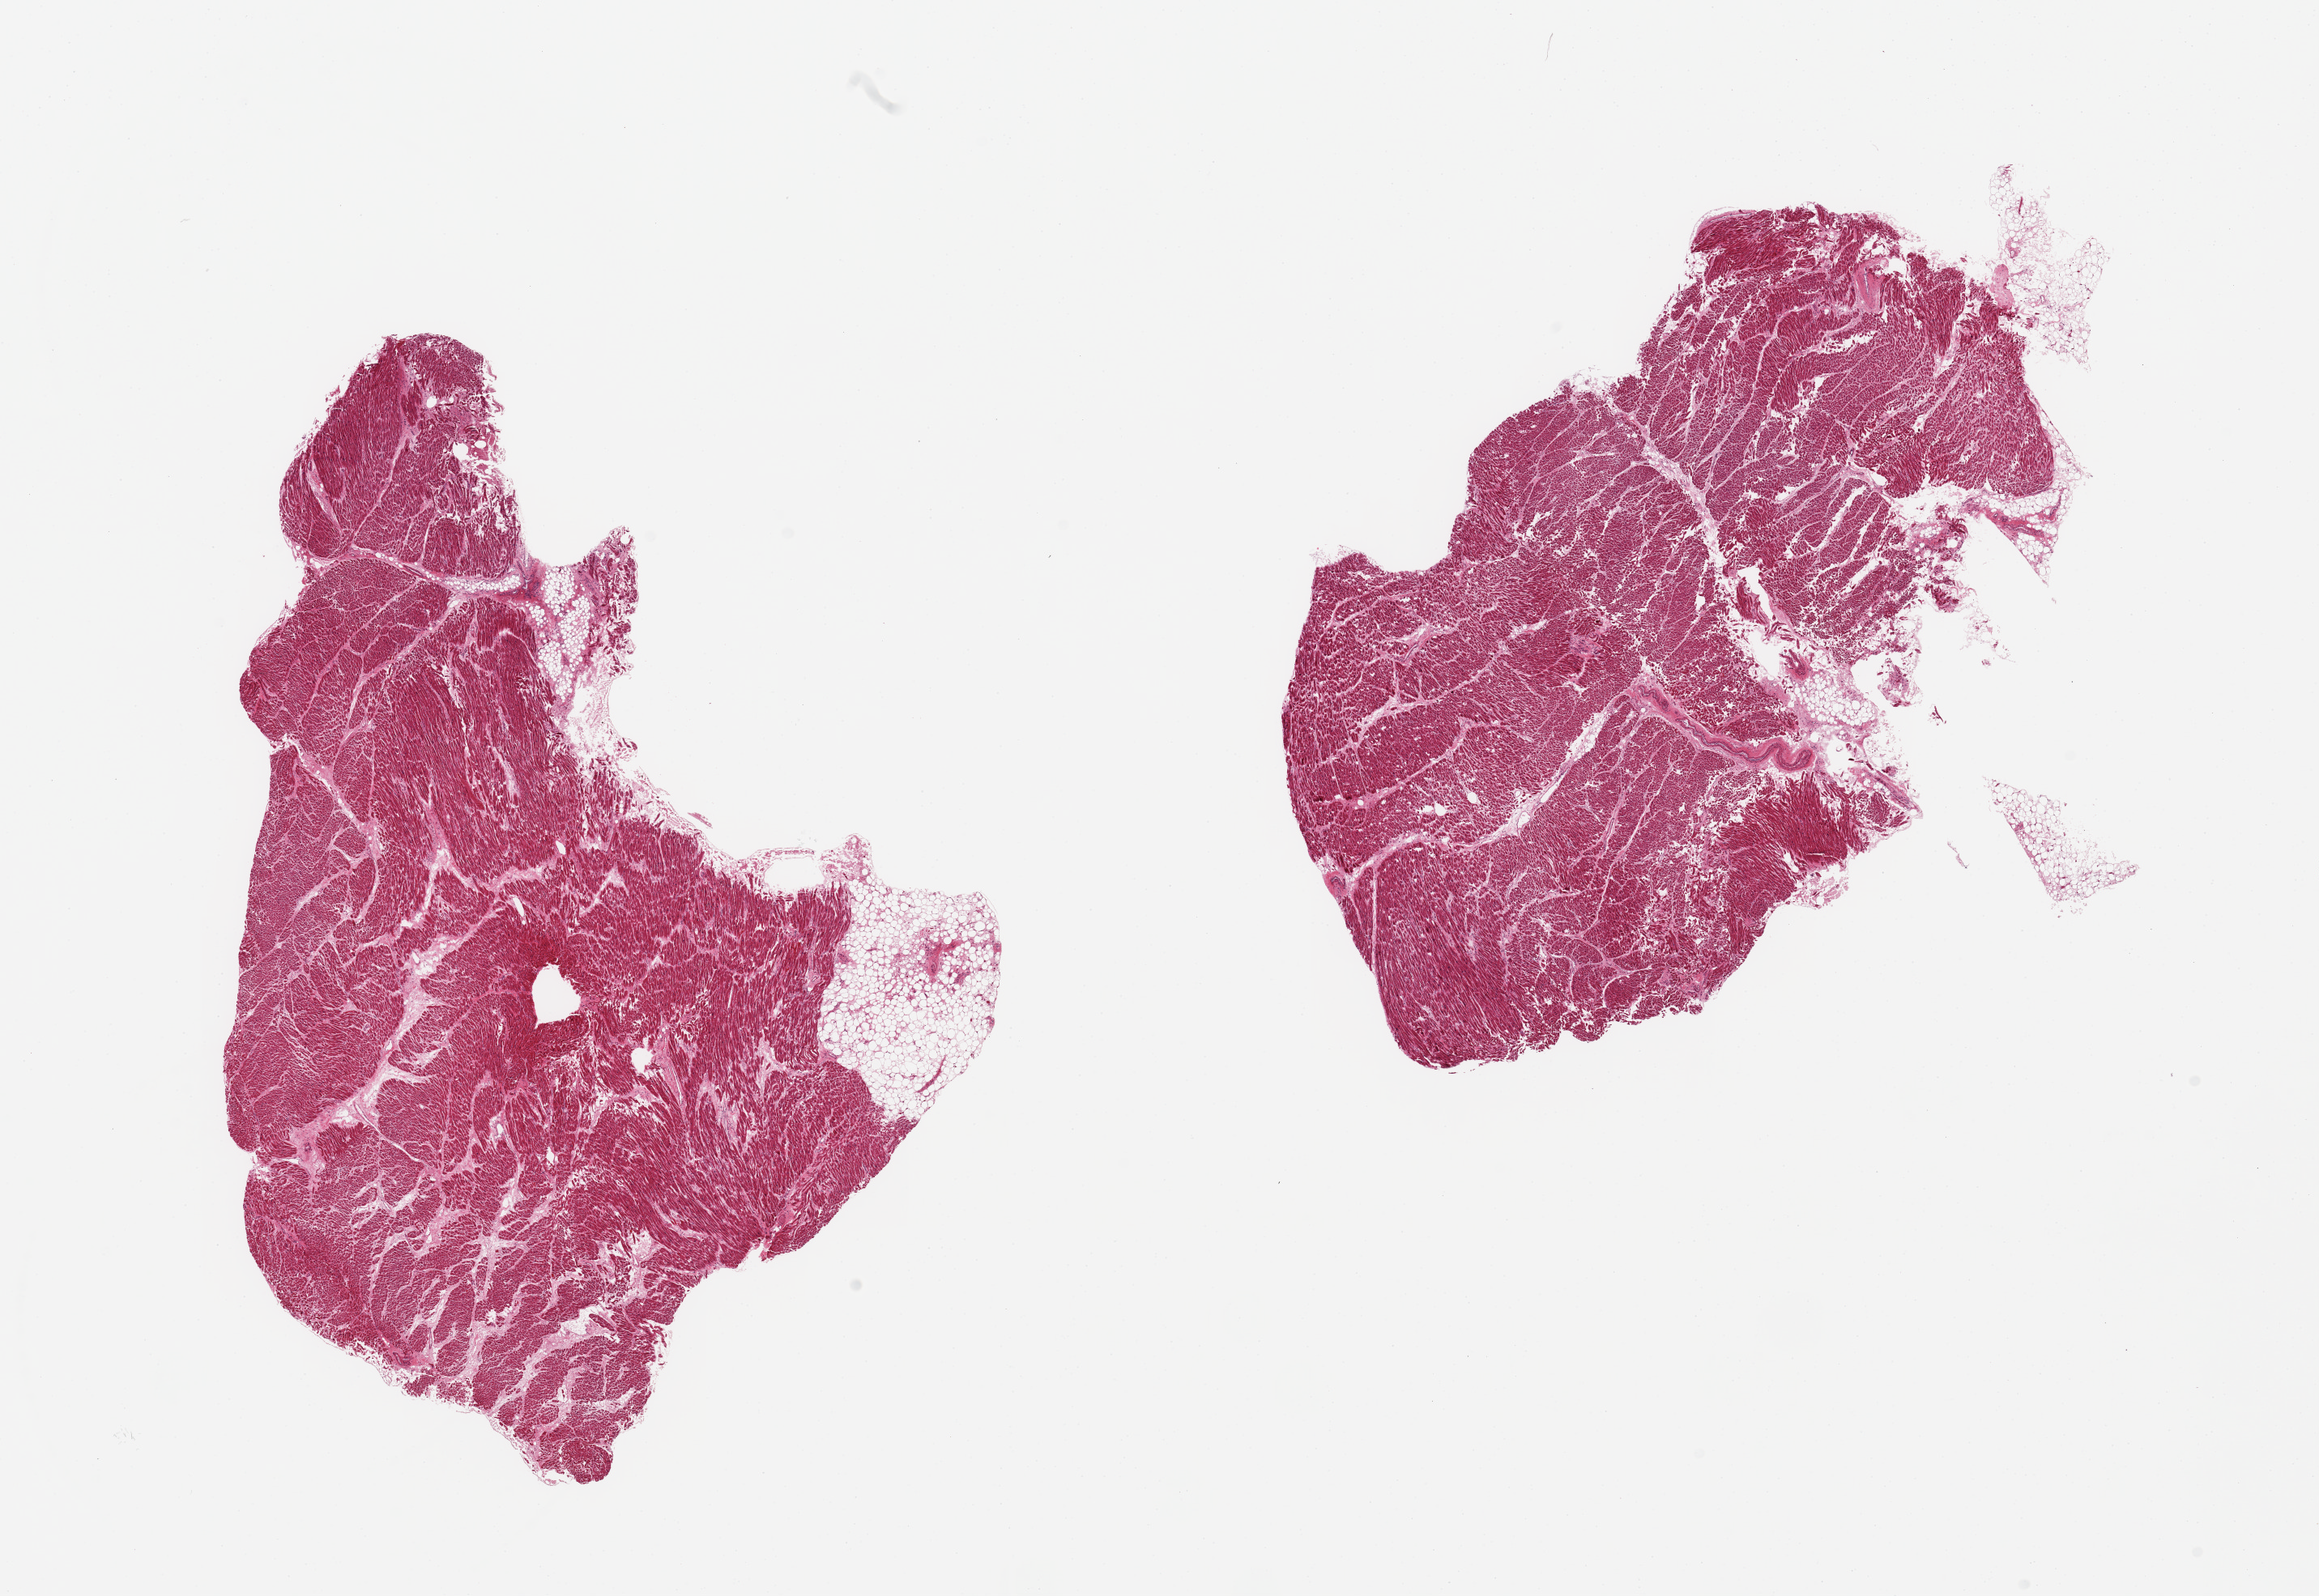
Hematoxylin and eosin (H&E) whole-slide image, brightfield, whole scanned area (about 22.6 x 15.6 mm) shown as a low-resolution overview. PAXgene-fixed paraffin-embedded (PFPE) section. Target tissue: heart. Tissue donor sample. Female donor.
Review note (as recorded): 2 pieces; 10% external fat.